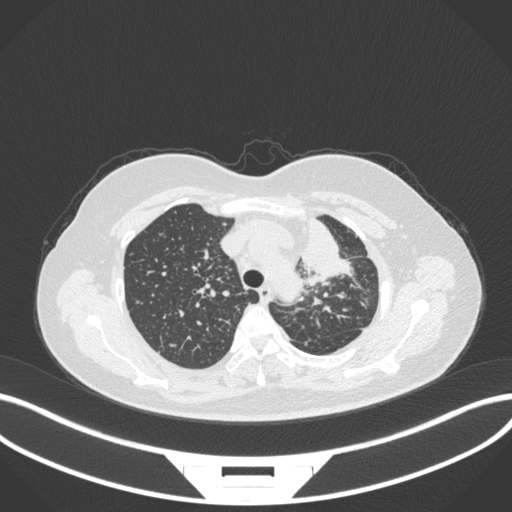
Chest CT, one axial slice. Slice 258 of 348 in the series (ordered by position). 120 kVp. Lung window (W 1500 / L -600 HU). 512 × 512 image matrix. Patient: female, 49 years. Case-level facts recorded for this patient, not image findings: clinical TNM (as recorded): T1c N0 M1.
Outlined on this slice (bounding box drawn by a radiologist):
- lung tumour (recorded histology: adenocarcinoma): bounding box [x1, y1, x2, y2] px = [294, 214, 356, 290]